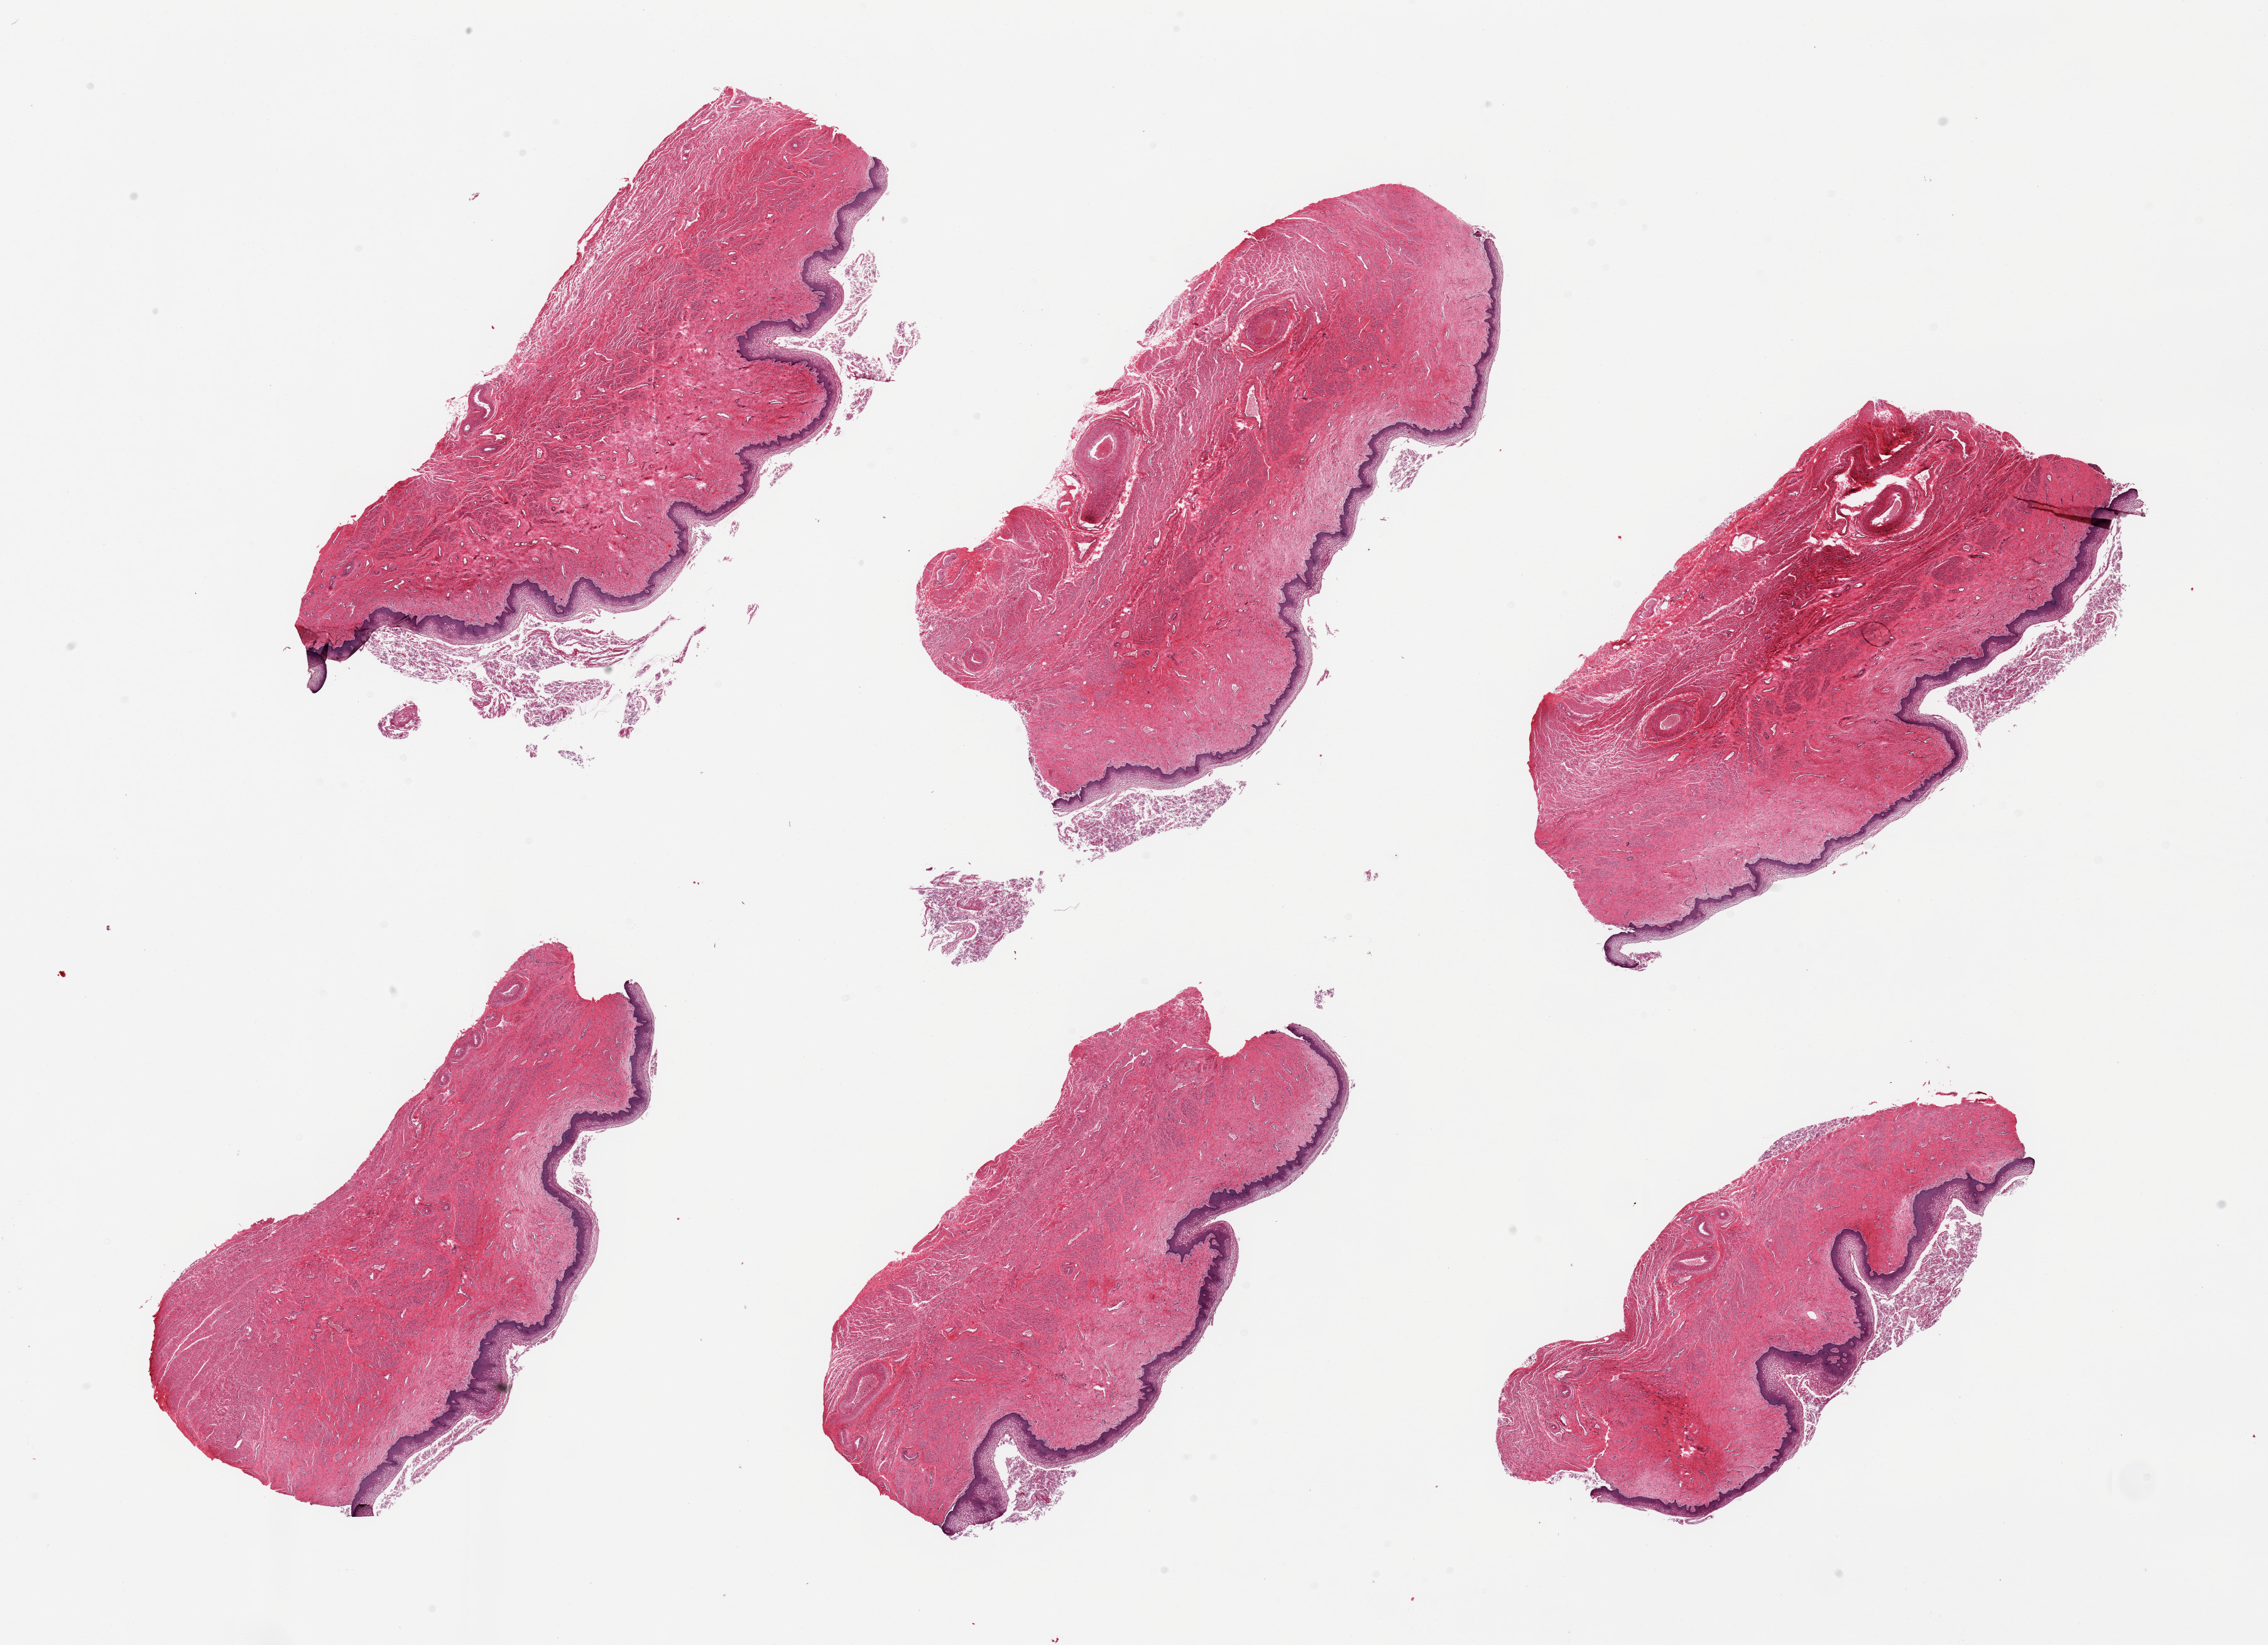
H&E whole-slide image, brightfield — shown as a low-resolution overview of the whole scanned area (about 28.5 x 20.7 mm), PAXgene-fixed, paraffin-embedded tissue, section of vagina (target tissue), tissue donor sample. Female donor.
* pathologist's review note for this sample: 6 pieces, squamous epithelium is ~0.2mm